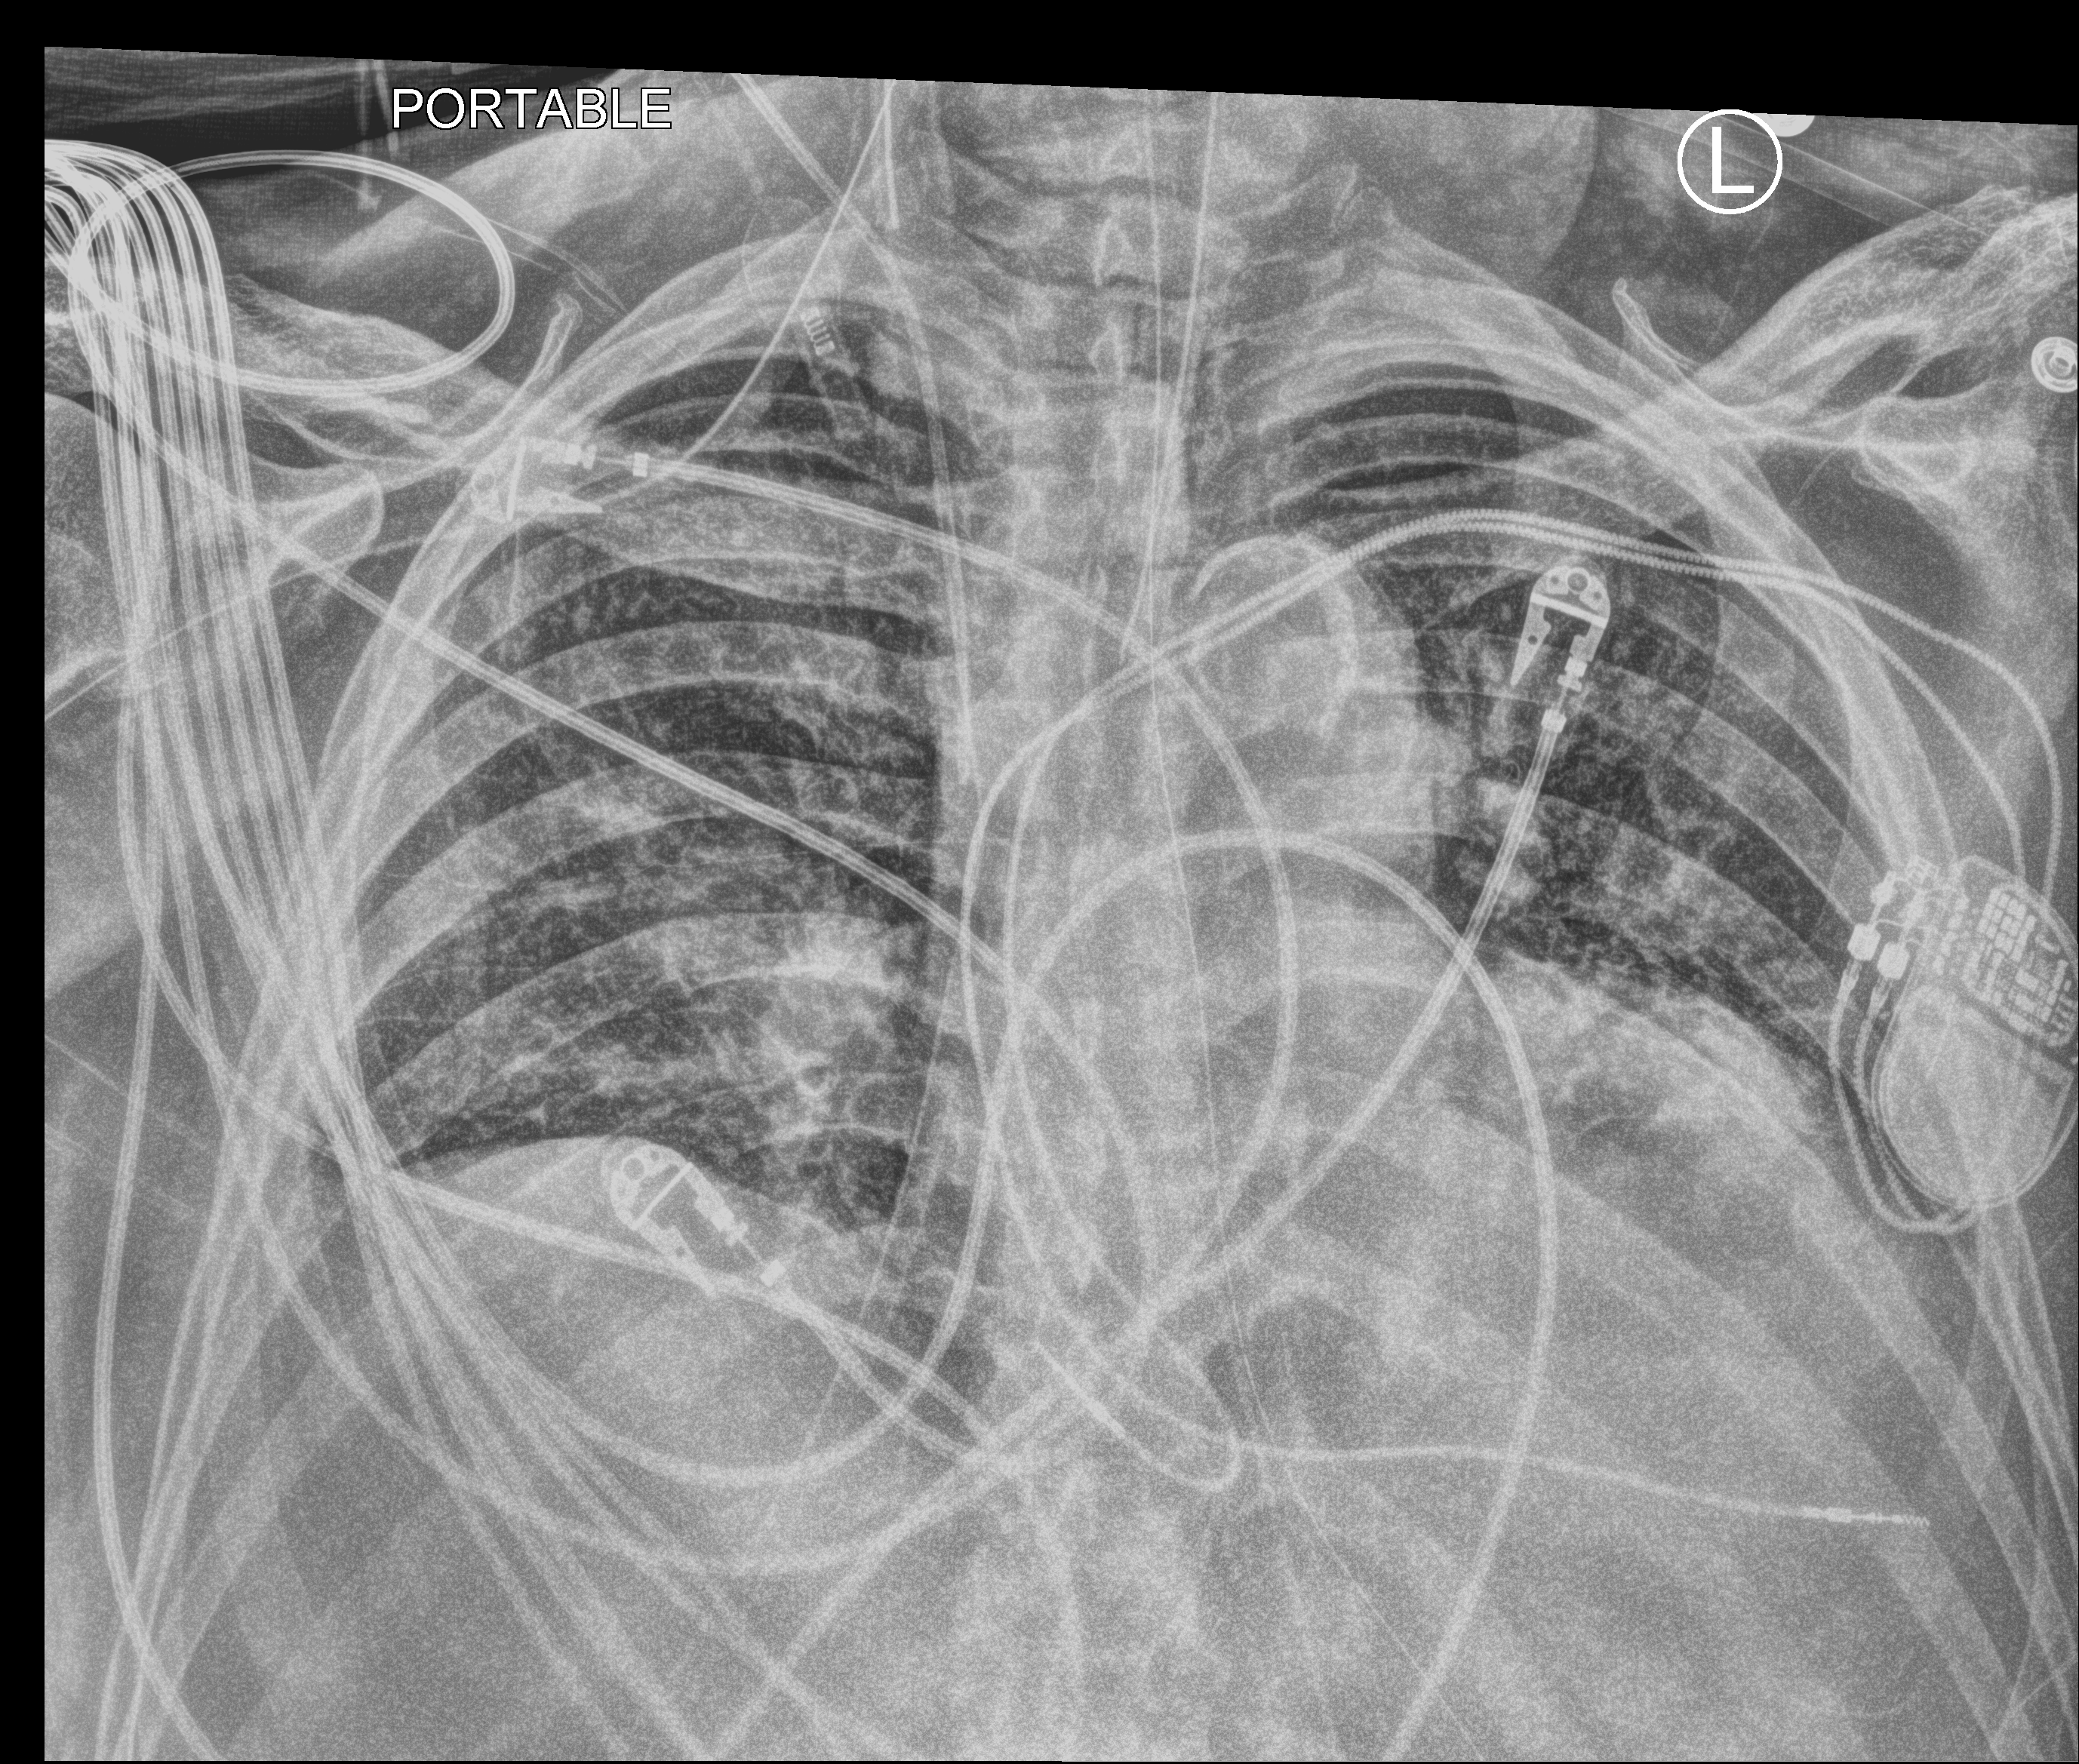
Chest X-ray (portable); anteroposterior (AP) projection. Male patient hospitalised with COVID-19, age 60–74 years.
Hospital-stay facts (about this admission, not read from this image; timing relative to this image not recorded):
- admitted to intensive care during this hospital stay: yes